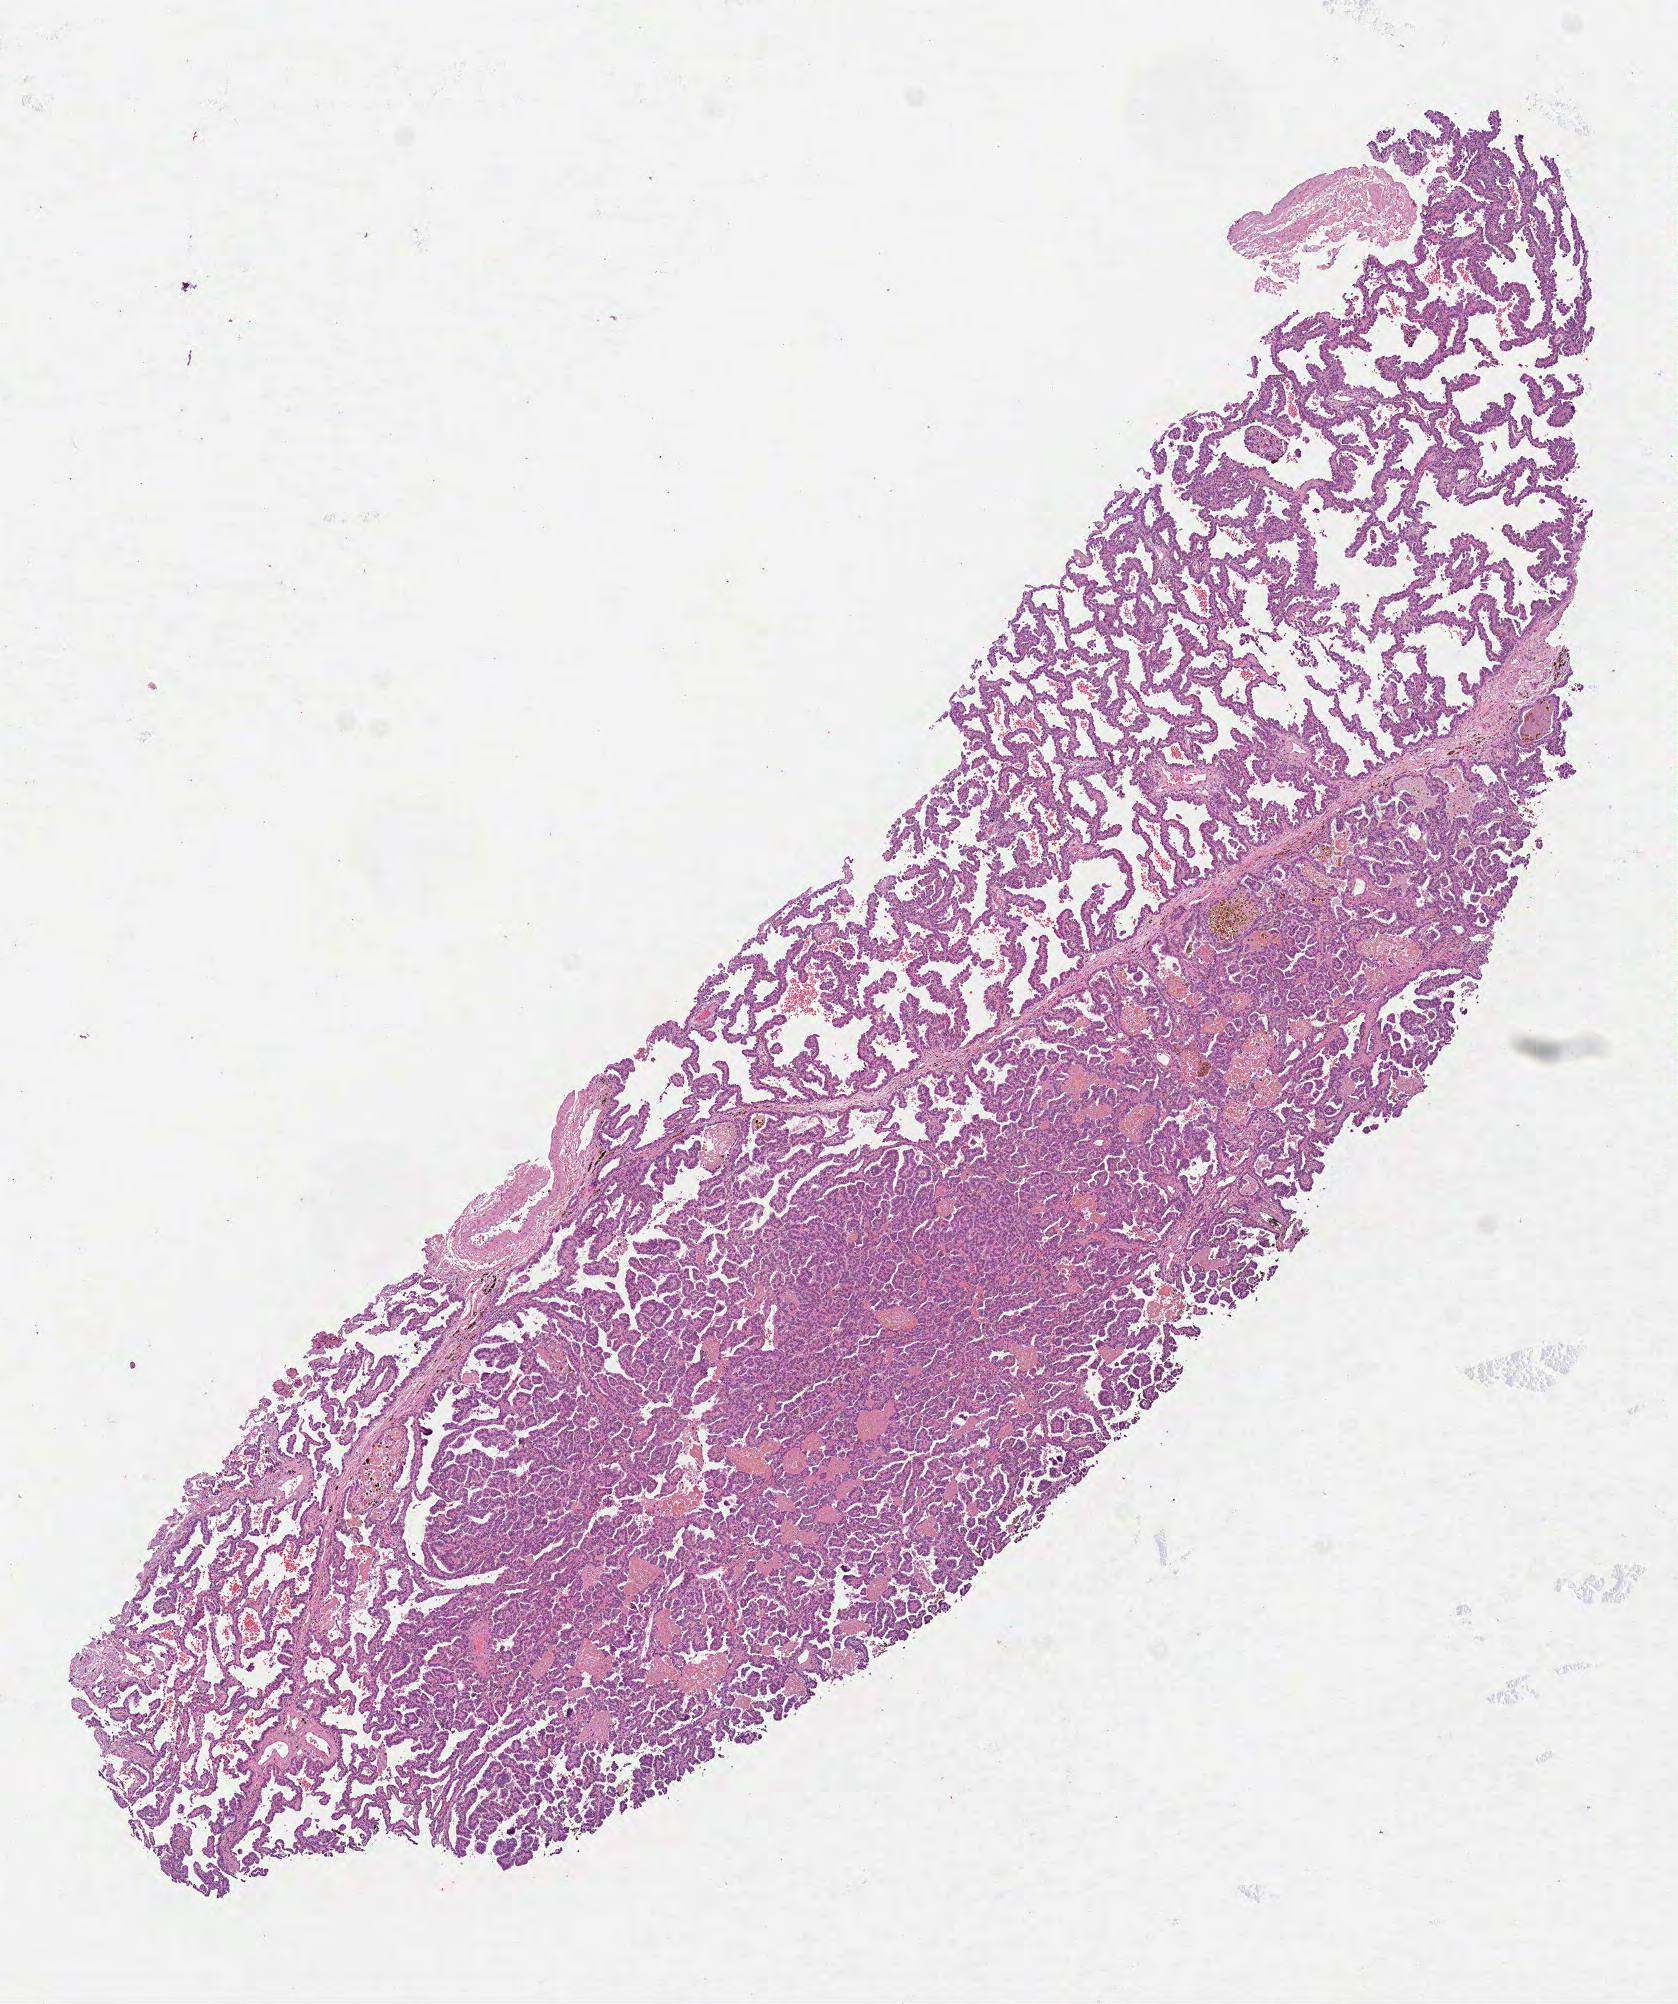
Whole-slide histology image, Hematoxylin and eosin (H&E) stained — low-resolution overview of the scanned area, about 6.8 x 8.1 mm (acquisition: 40x scan), formalin-fixed paraffin-embedded (FFPE) diagnostic section, primary tumour sample from the lung. Male patient; age at initial diagnosis 72 years.
* histologic diagnosis: Papillary adenocarcinoma, NOS (upper lobe, lung)
* AJCC pathologic stage: IB (6th edition)
* laterality: right